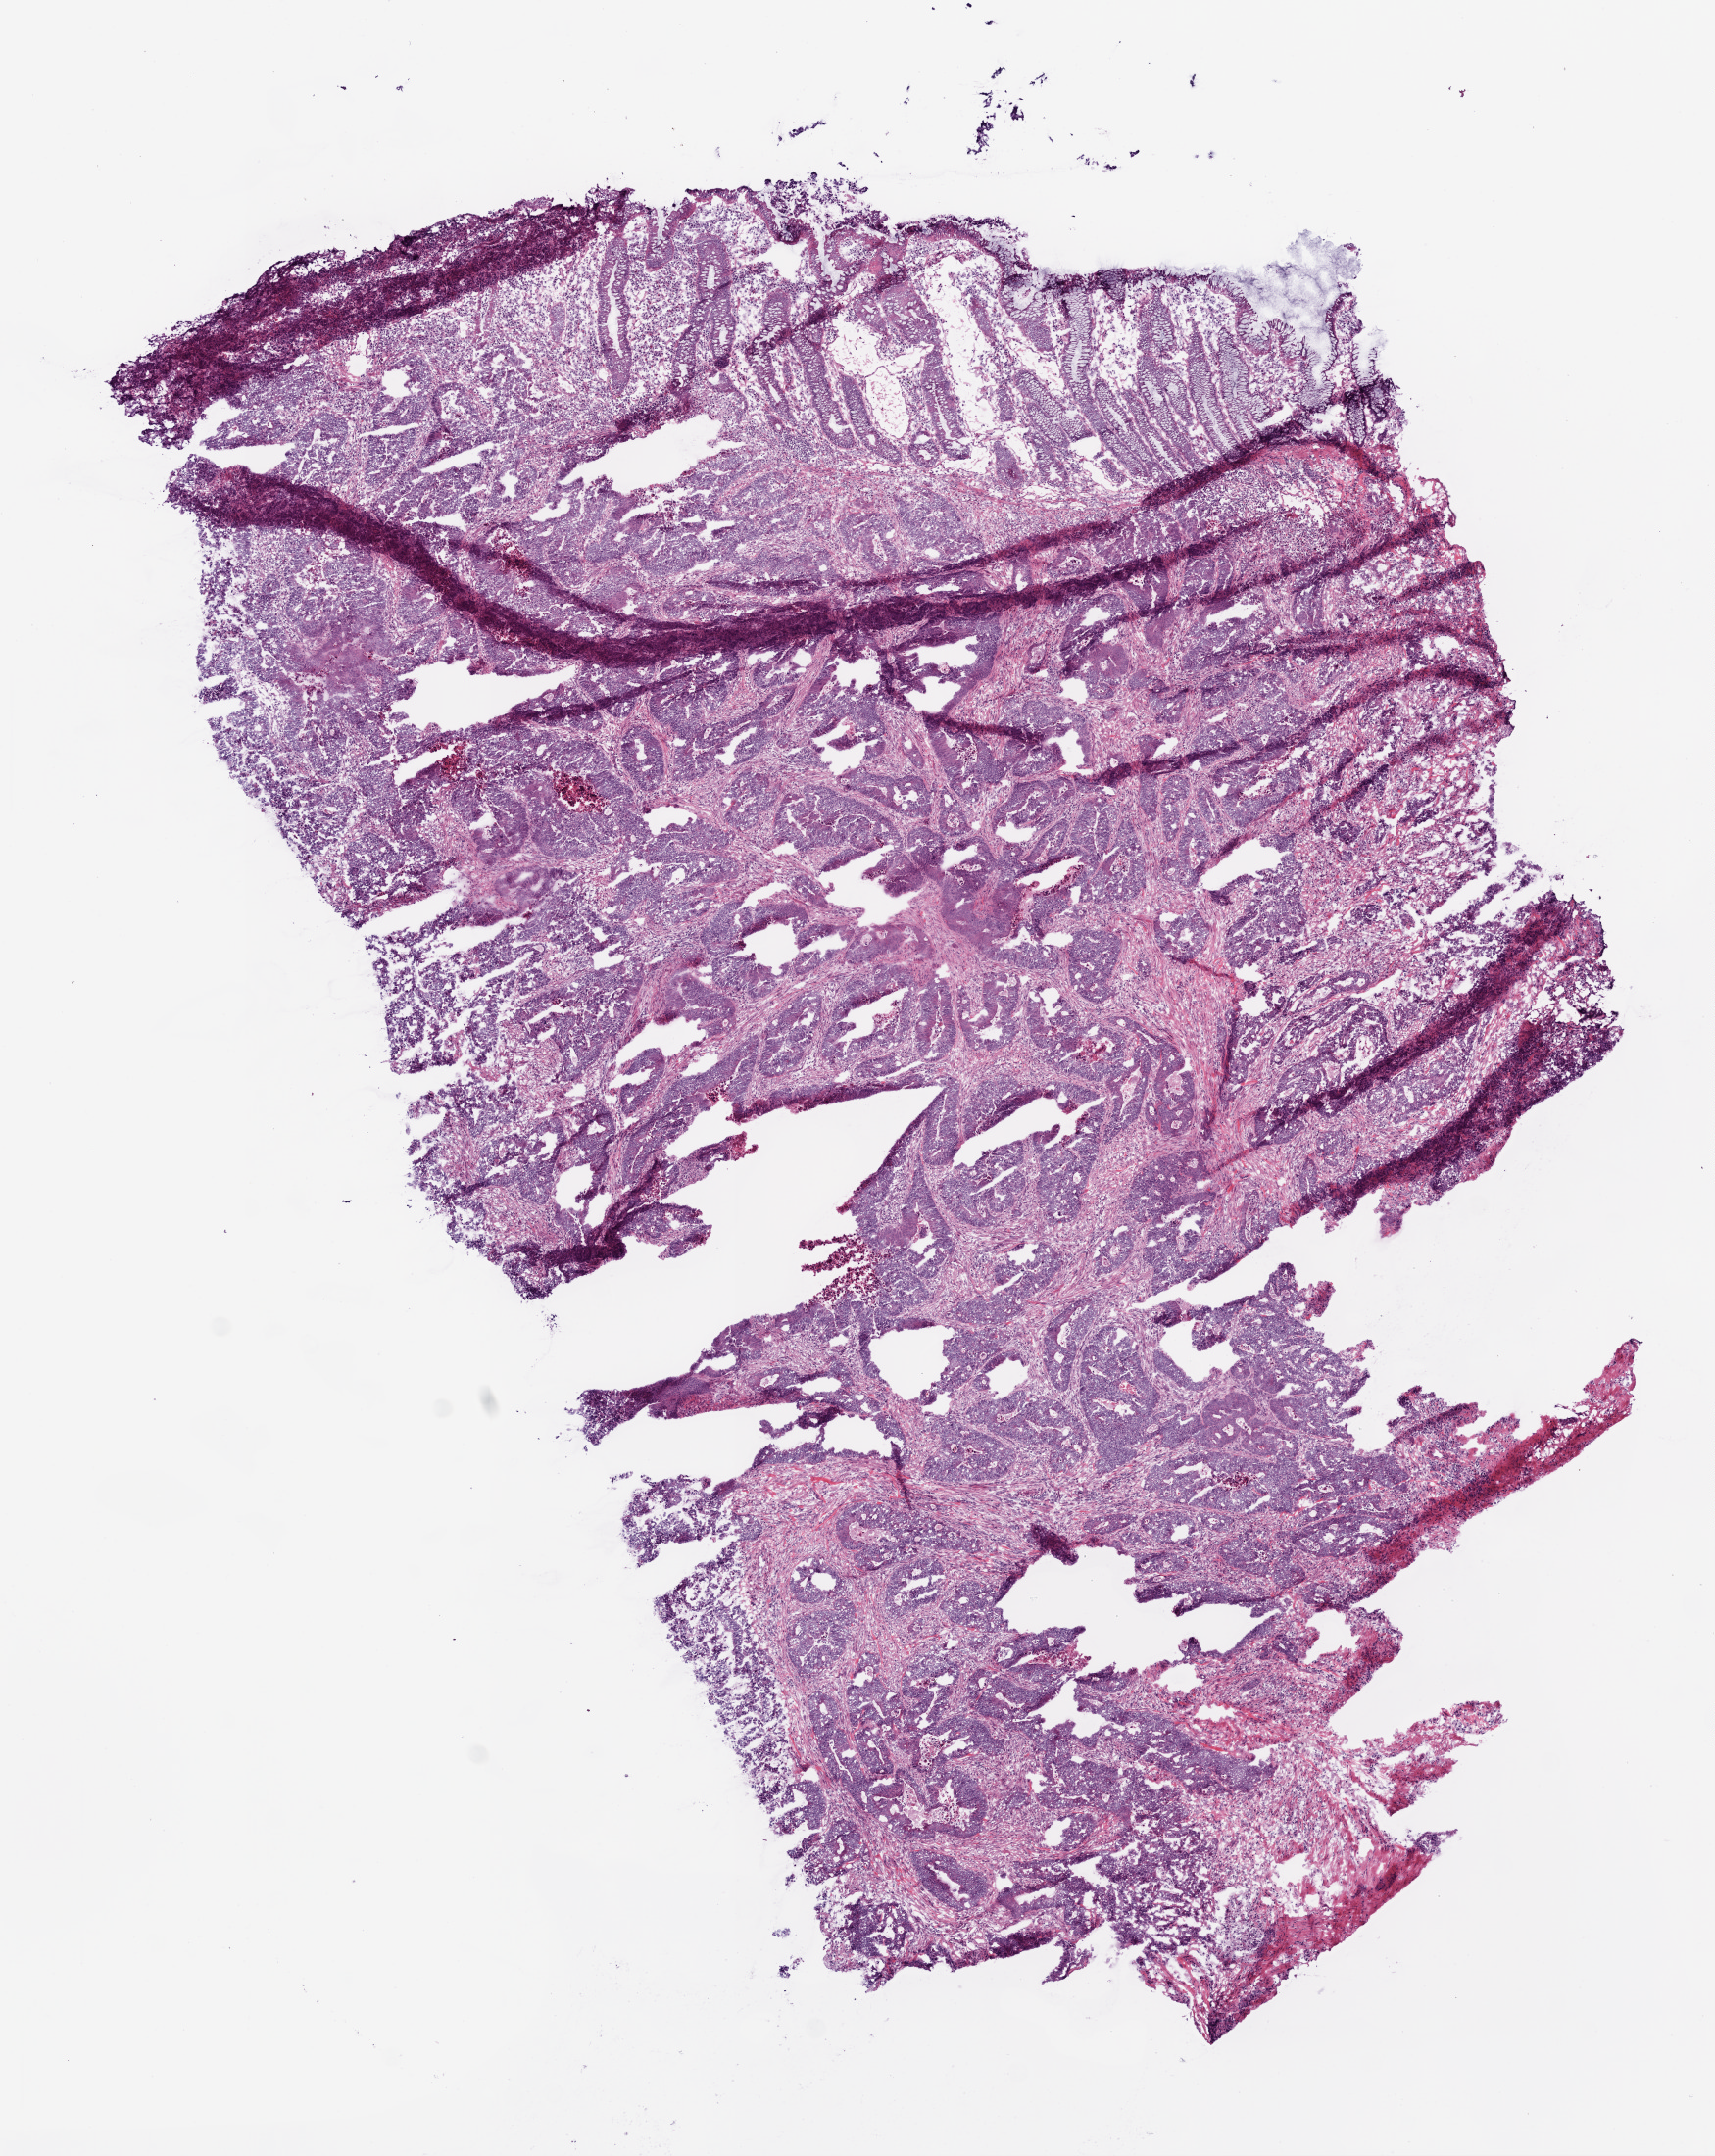
H&E-stained whole-slide image, shown as a low-resolution overview of the whole scanned area (about 7.0 x 8.8 mm, acquisition: 20x scan), frozen section from the bottom of the tissue portion, primary tumour sample from the rectum. Male patient; age at initial diagnosis 75 years. Composition of this section per pathologist review: tumour cells 72%, tumour nuclei 70%, normal cells 10%, stromal cells 10%, necrosis 8%.
- AJCC pathologic stage: IV (6th edition)
- TNM: T3 N1 M1
- diagnosis: Adenocarcinoma, NOS (colon, NOS)